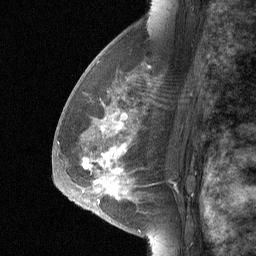
Breast MRI (dynamic contrast-enhanced), one sagittal slice. Slice 39 of 64 in the series (ordered by position). Dynamic contrast-enhanced study with each time point stored as its own series, time point 2 of 3 at this slice position (early post-contrast, ordered by acquisition time). 1.5 T. TE 4.8 ms, TR 27 ms. 256 × 256 image matrix, field of view 180 × 180 mm. Patient: female, 56 years. From the clinical record (not read from this slice): setting: breast cancer imaged before/during neoadjuvant chemotherapy; receptor status: HER2-positive.
Annotated regions visible in this slice (semi-automatically segmented with operator editing):
- analysis volume of interest (the breast-tissue region the enhancement analysis was run in; not a lesion): bounding box [x1, y1, x2, y2] px = [68, 83, 161, 214]
- tumour enhancement mask (voxels above the 90 % enhancement threshold inside the analysis volume of interest): [86, 125, 124, 191]